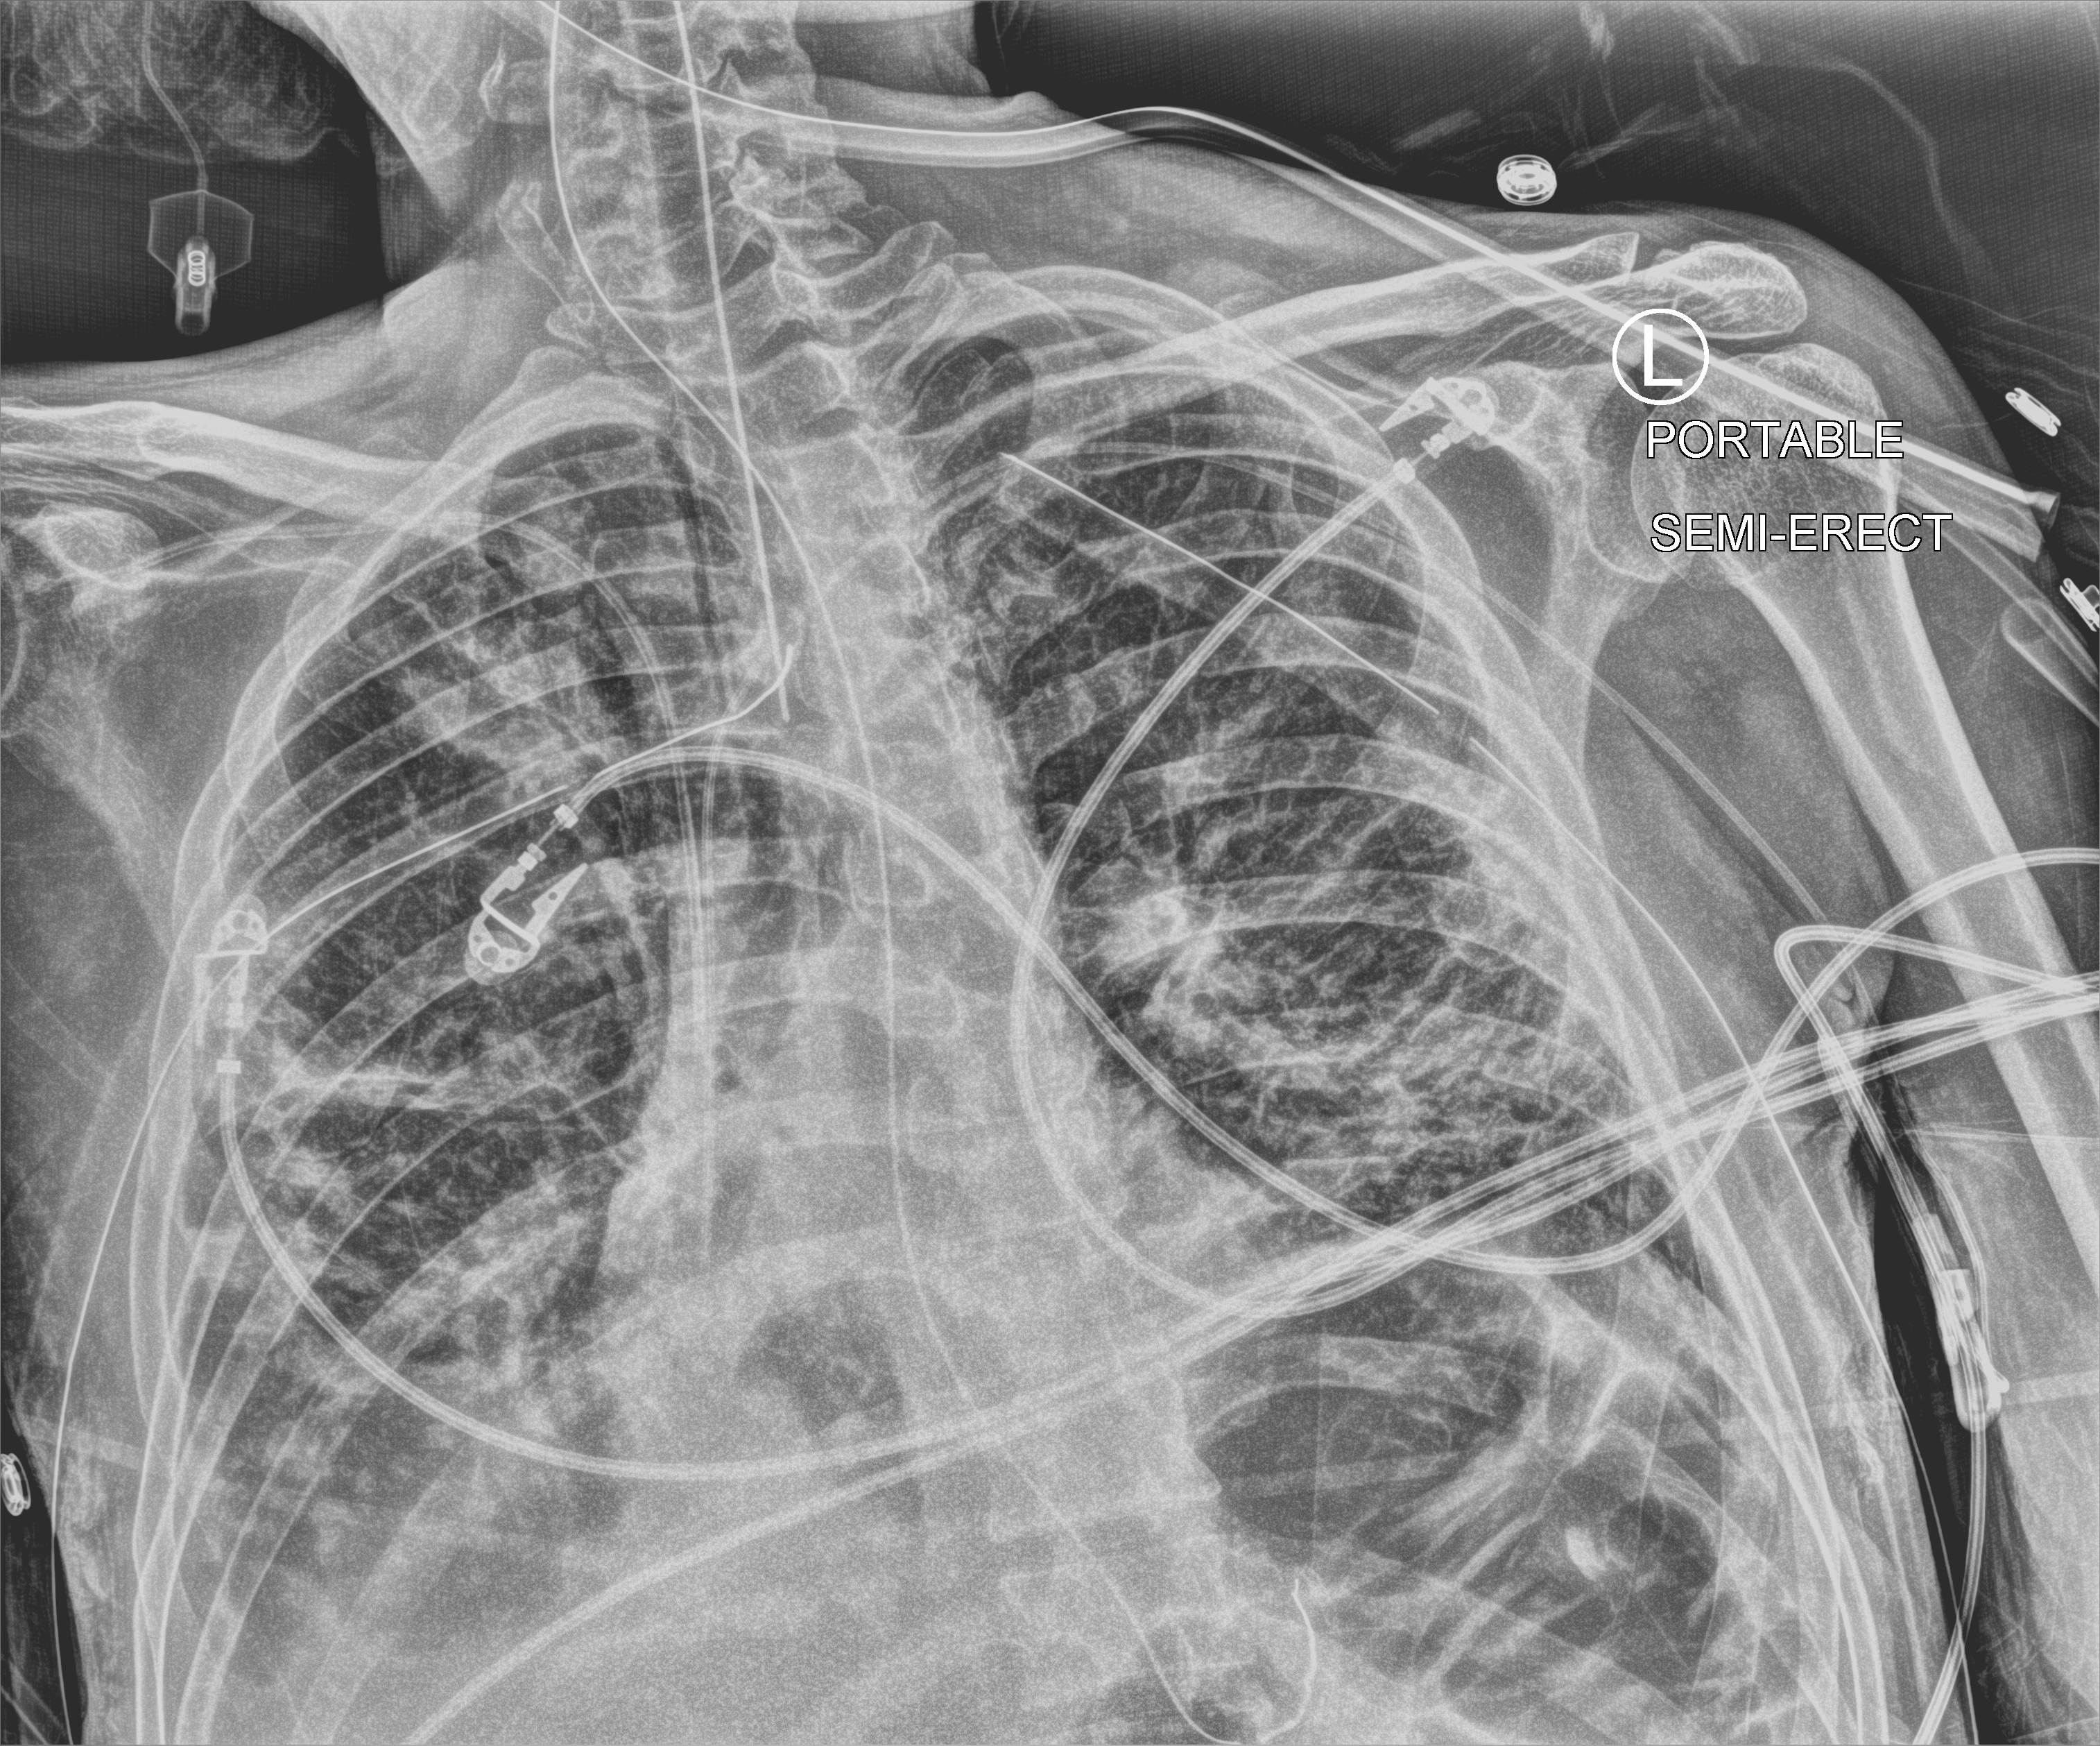
Bedside chest radiograph (computed radiography), anteroposterior (AP) projection. Patient hospitalised with COVID-19; male, aged 18–59 years.
Hospital-stay facts (about this admission, not read from this image; timing relative to this image not recorded):
- length of hospital stay: 96 days